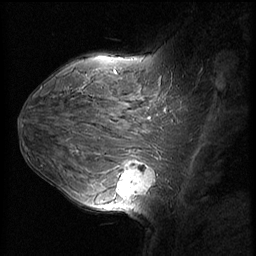
Breast MRI (dynamic contrast-enhanced), one sagittal slice. Position 40 of 60 along the scan axis. Dynamic contrast-enhanced series, image 2 of 3 at this slice position (ordered by acquisition). 1.5 T. TE 4.2 ms, TR 8.9 ms. 2.5 mm slice thickness. 256 × 256 image matrix, field of view 220 × 220 mm. Female patient, age 37 years. From the clinical record (not read from this slice): setting: breast cancer imaged before/during neoadjuvant chemotherapy; receptor status: triple-negative.
Outlined on this slice (semi-automatically segmented with operator editing):
- analysis volume of interest (the breast-tissue region the enhancement analysis was run in; not a lesion): bounding box [x1, y1, x2, y2] px = [114, 153, 159, 206]
- tumour enhancement mask (voxels above the 140 % enhancement threshold inside the analysis volume of interest): [118, 162, 155, 199]